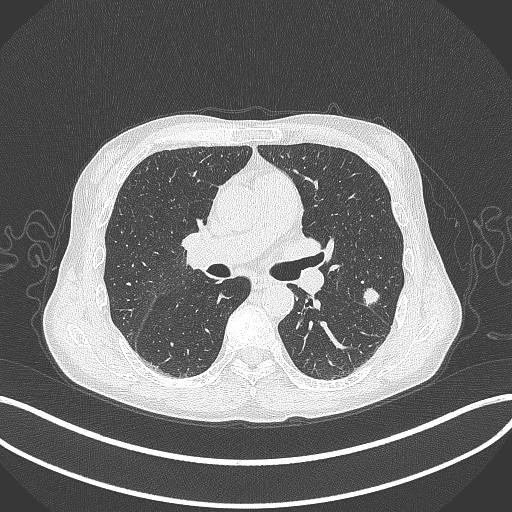
Chest CT, one axial slice. Slice 207 of 429 in the series (ordered by position). Reconstruction kernel B70f. Lung window (W 1500 / L -600 HU). 1 mm slice thickness. 512 × 512 image matrix, field of view 400 × 400 mm. Patient: male, 58 years. Case-level facts recorded for this patient, not image findings: clinical TNM (as recorded): T1c N0 M0; histopathological grade: G2.
Annotated regions visible in this slice (rectangle marked by the reading radiologist):
- lung tumour (recorded histology: adenocarcinoma): bounding box [x1, y1, x2, y2] px = [362, 286, 381, 307]